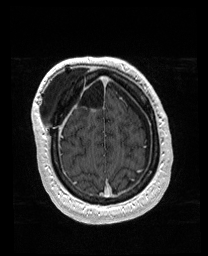
Brain MRI from a brain-tumour surgery series, one axial slice. Position 41 of 176 along the scan axis. T1-weighted post-contrast. 208 × 256 image matrix, field of view 208 × 256 mm. From the clinical record (not read from this slice): histopathology: Astrocytoma; WHO grade: 4; IDH mutation: yes; tumour location: Right Orbitofrontal Anterior Temporal Insular.
Structures marked on this image (expert manual segmentation):
- previous resection cavity: bounding box (x1, y1, x2, y2) in pixels: (70, 76, 95, 107)